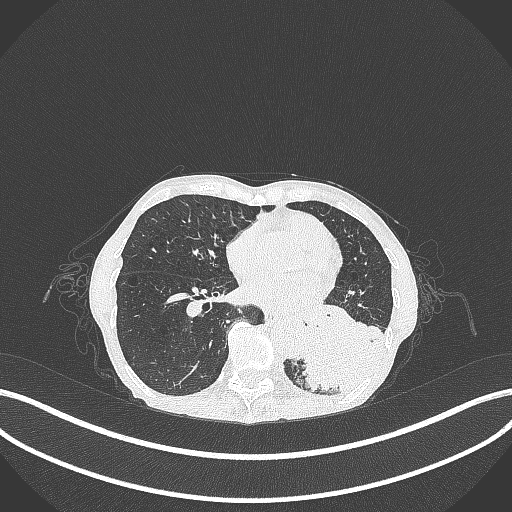
Chest CT, one axial slice. Reconstruction kernel B70f. Lung window (W 1500 / L -600 HU). 1 mm slice thickness. 512 × 512 image matrix. Patient: female, 70 years. Case-level facts recorded for this patient, not image findings: clinical TNM (as recorded): T3 N0 M0; histopathological grade: G3.
Outlined on this slice (rectangle marked by the reading radiologist):
- lung tumour (recorded histology: small cell carcinoma): box from (x=284, y=309) to (x=395, y=399) px